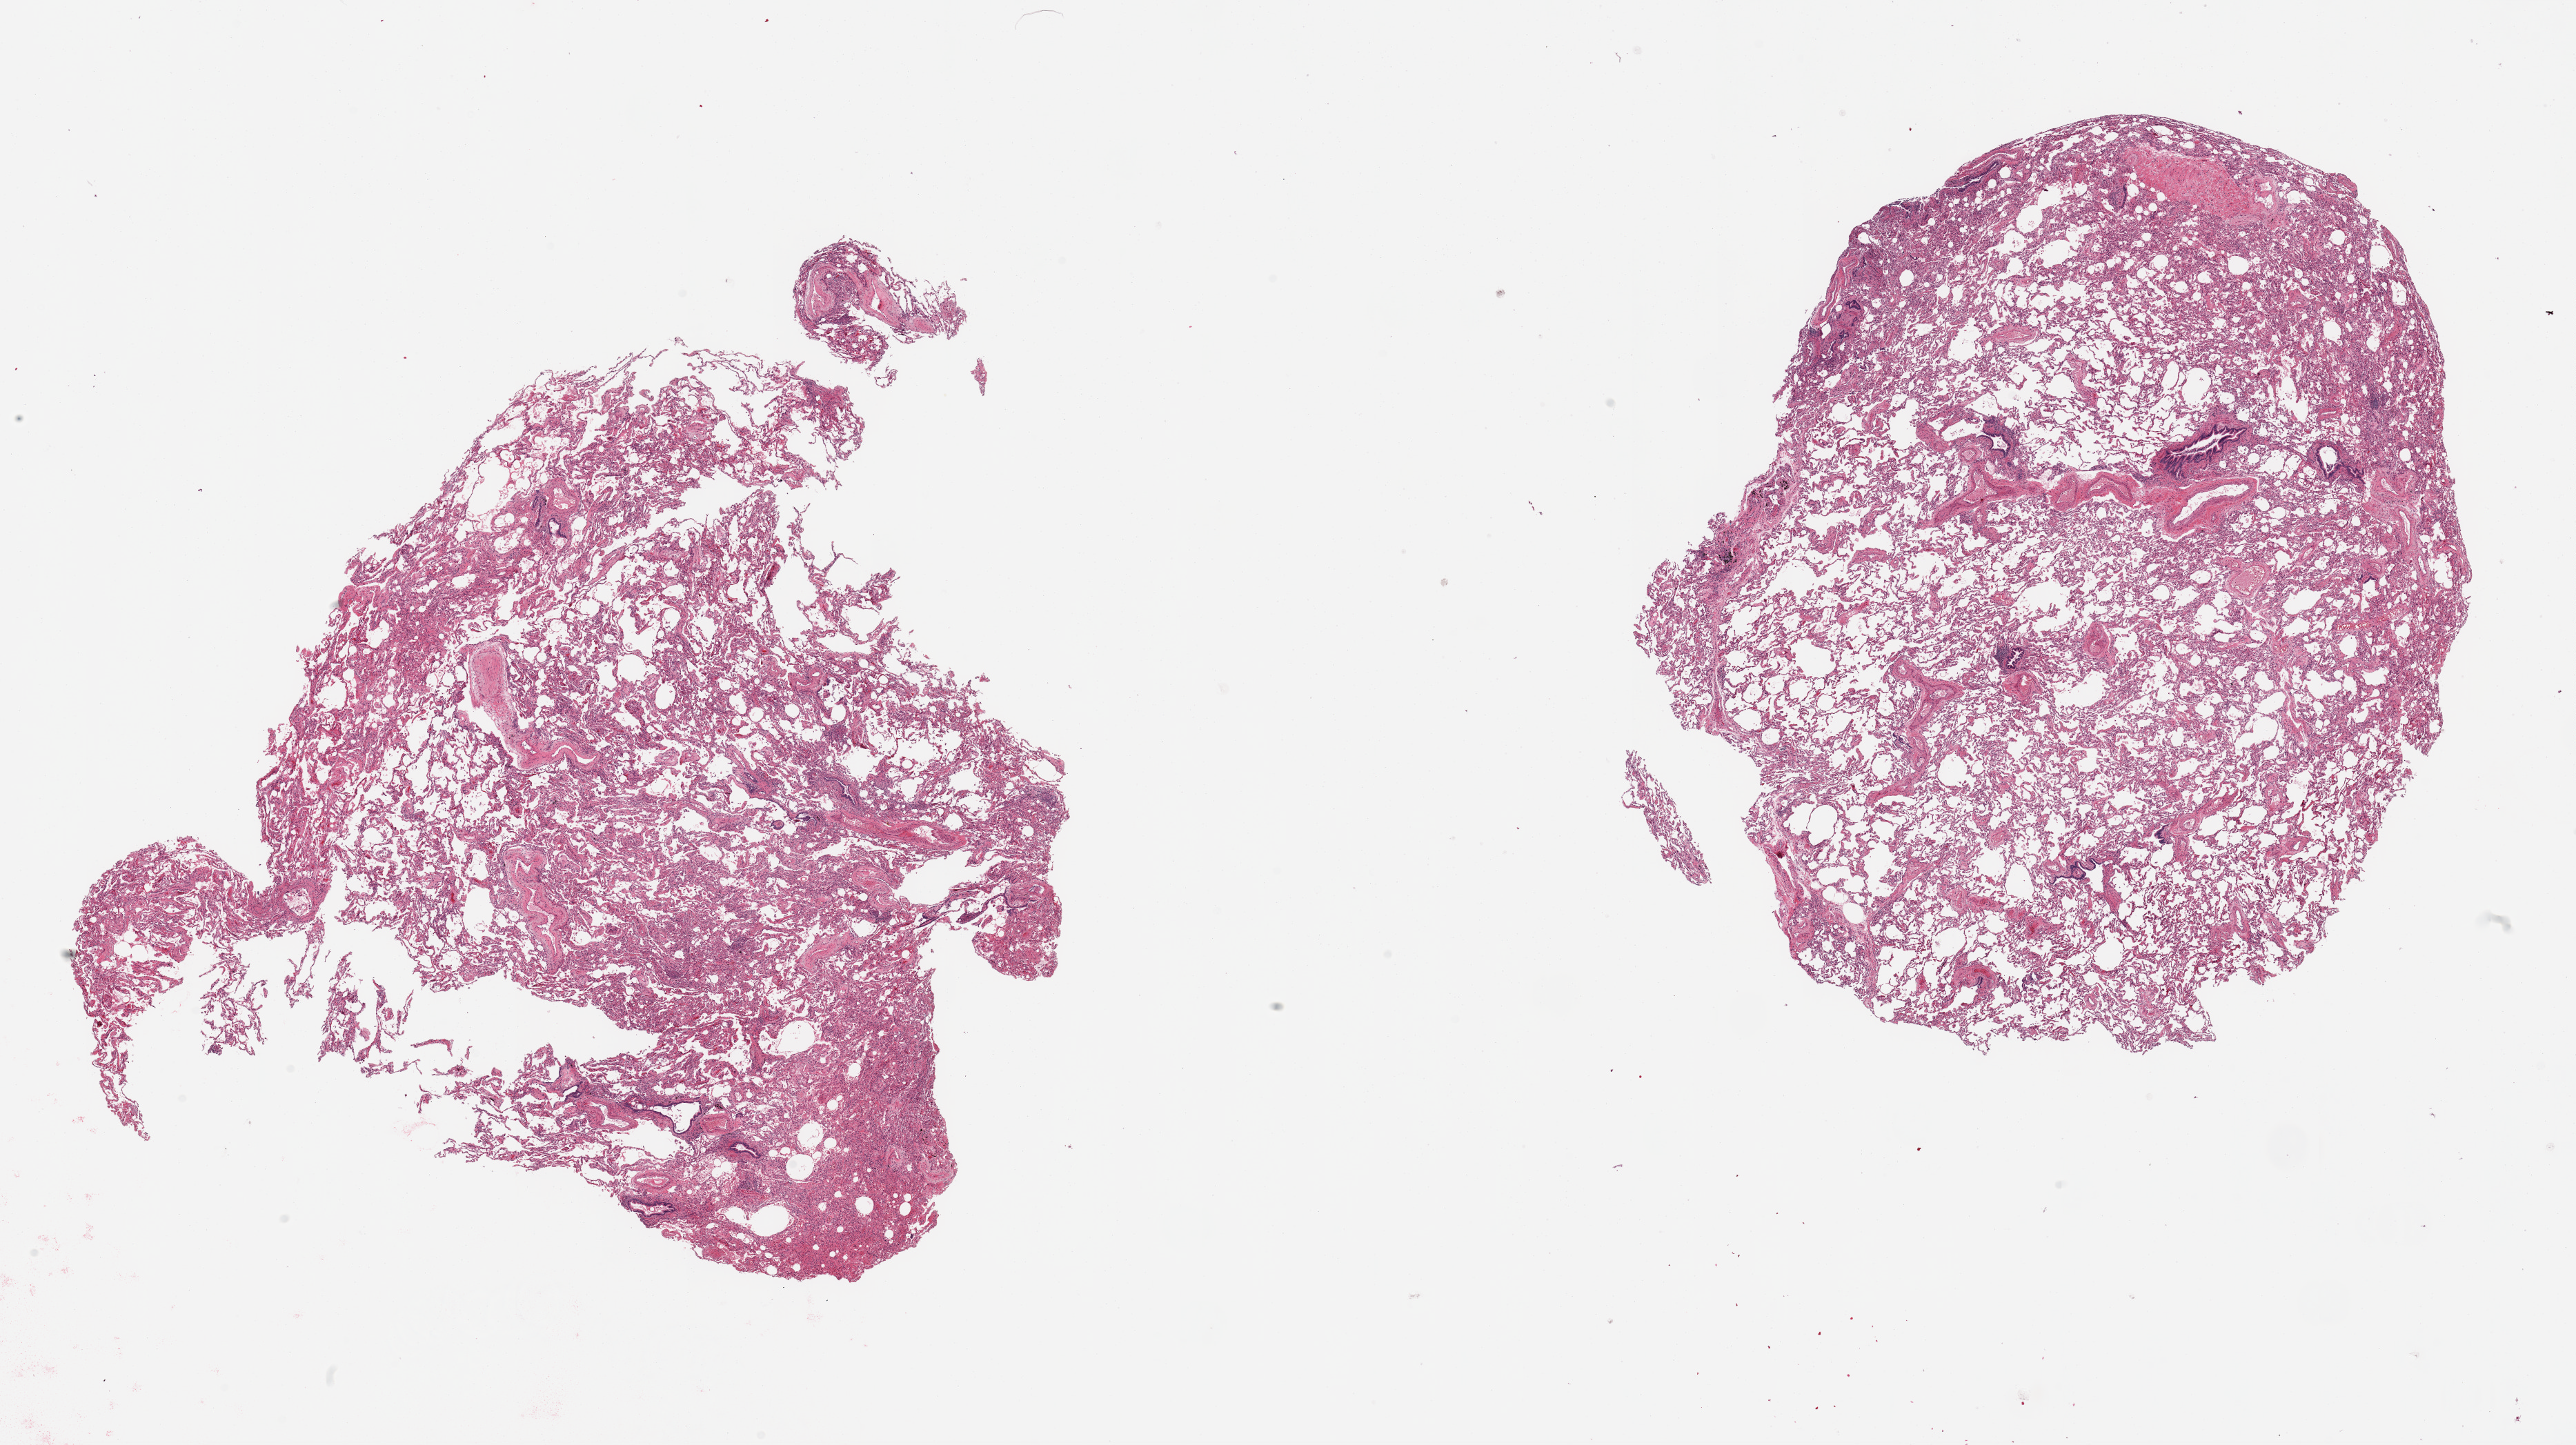
H&E whole-slide image — low-resolution overview of the scanned area, about 29.5 x 16.6 mm (acquisition: 20x scan). PAXgene-fixed, paraffin-embedded tissue. Section of lung (target tissue). Donor tissue sample. Female donor.
Reviewer comment on this tissue sample: 2 pieces, minimal congestion.